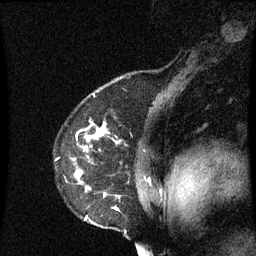
Breast MRI (dynamic contrast-enhanced), one sagittal slice. Slice 50 of 60 in the series (ordered by position). Dynamic contrast-enhanced series, image 2 of 3 at this slice position (ordered by acquisition). 1.5 T. TE 4.2 ms, TR 8.9 ms. 256 × 256 image matrix, field of view 200 × 200 mm. Female patient, age 53 years. Case-level facts recorded for this patient, not image findings: setting: breast cancer imaged before/during neoadjuvant chemotherapy; receptor status: HR-positive, HER2-negative.
Outlined on this slice (semi-automatically segmented with operator editing):
- analysis volume of interest (the breast-tissue region the enhancement analysis was run in; not a lesion): bounding box [x1, y1, x2, y2] px = [66, 128, 157, 231]
- tumour enhancement mask (voxels above the 70 % enhancement threshold inside the analysis volume of interest): [76, 130, 119, 219]